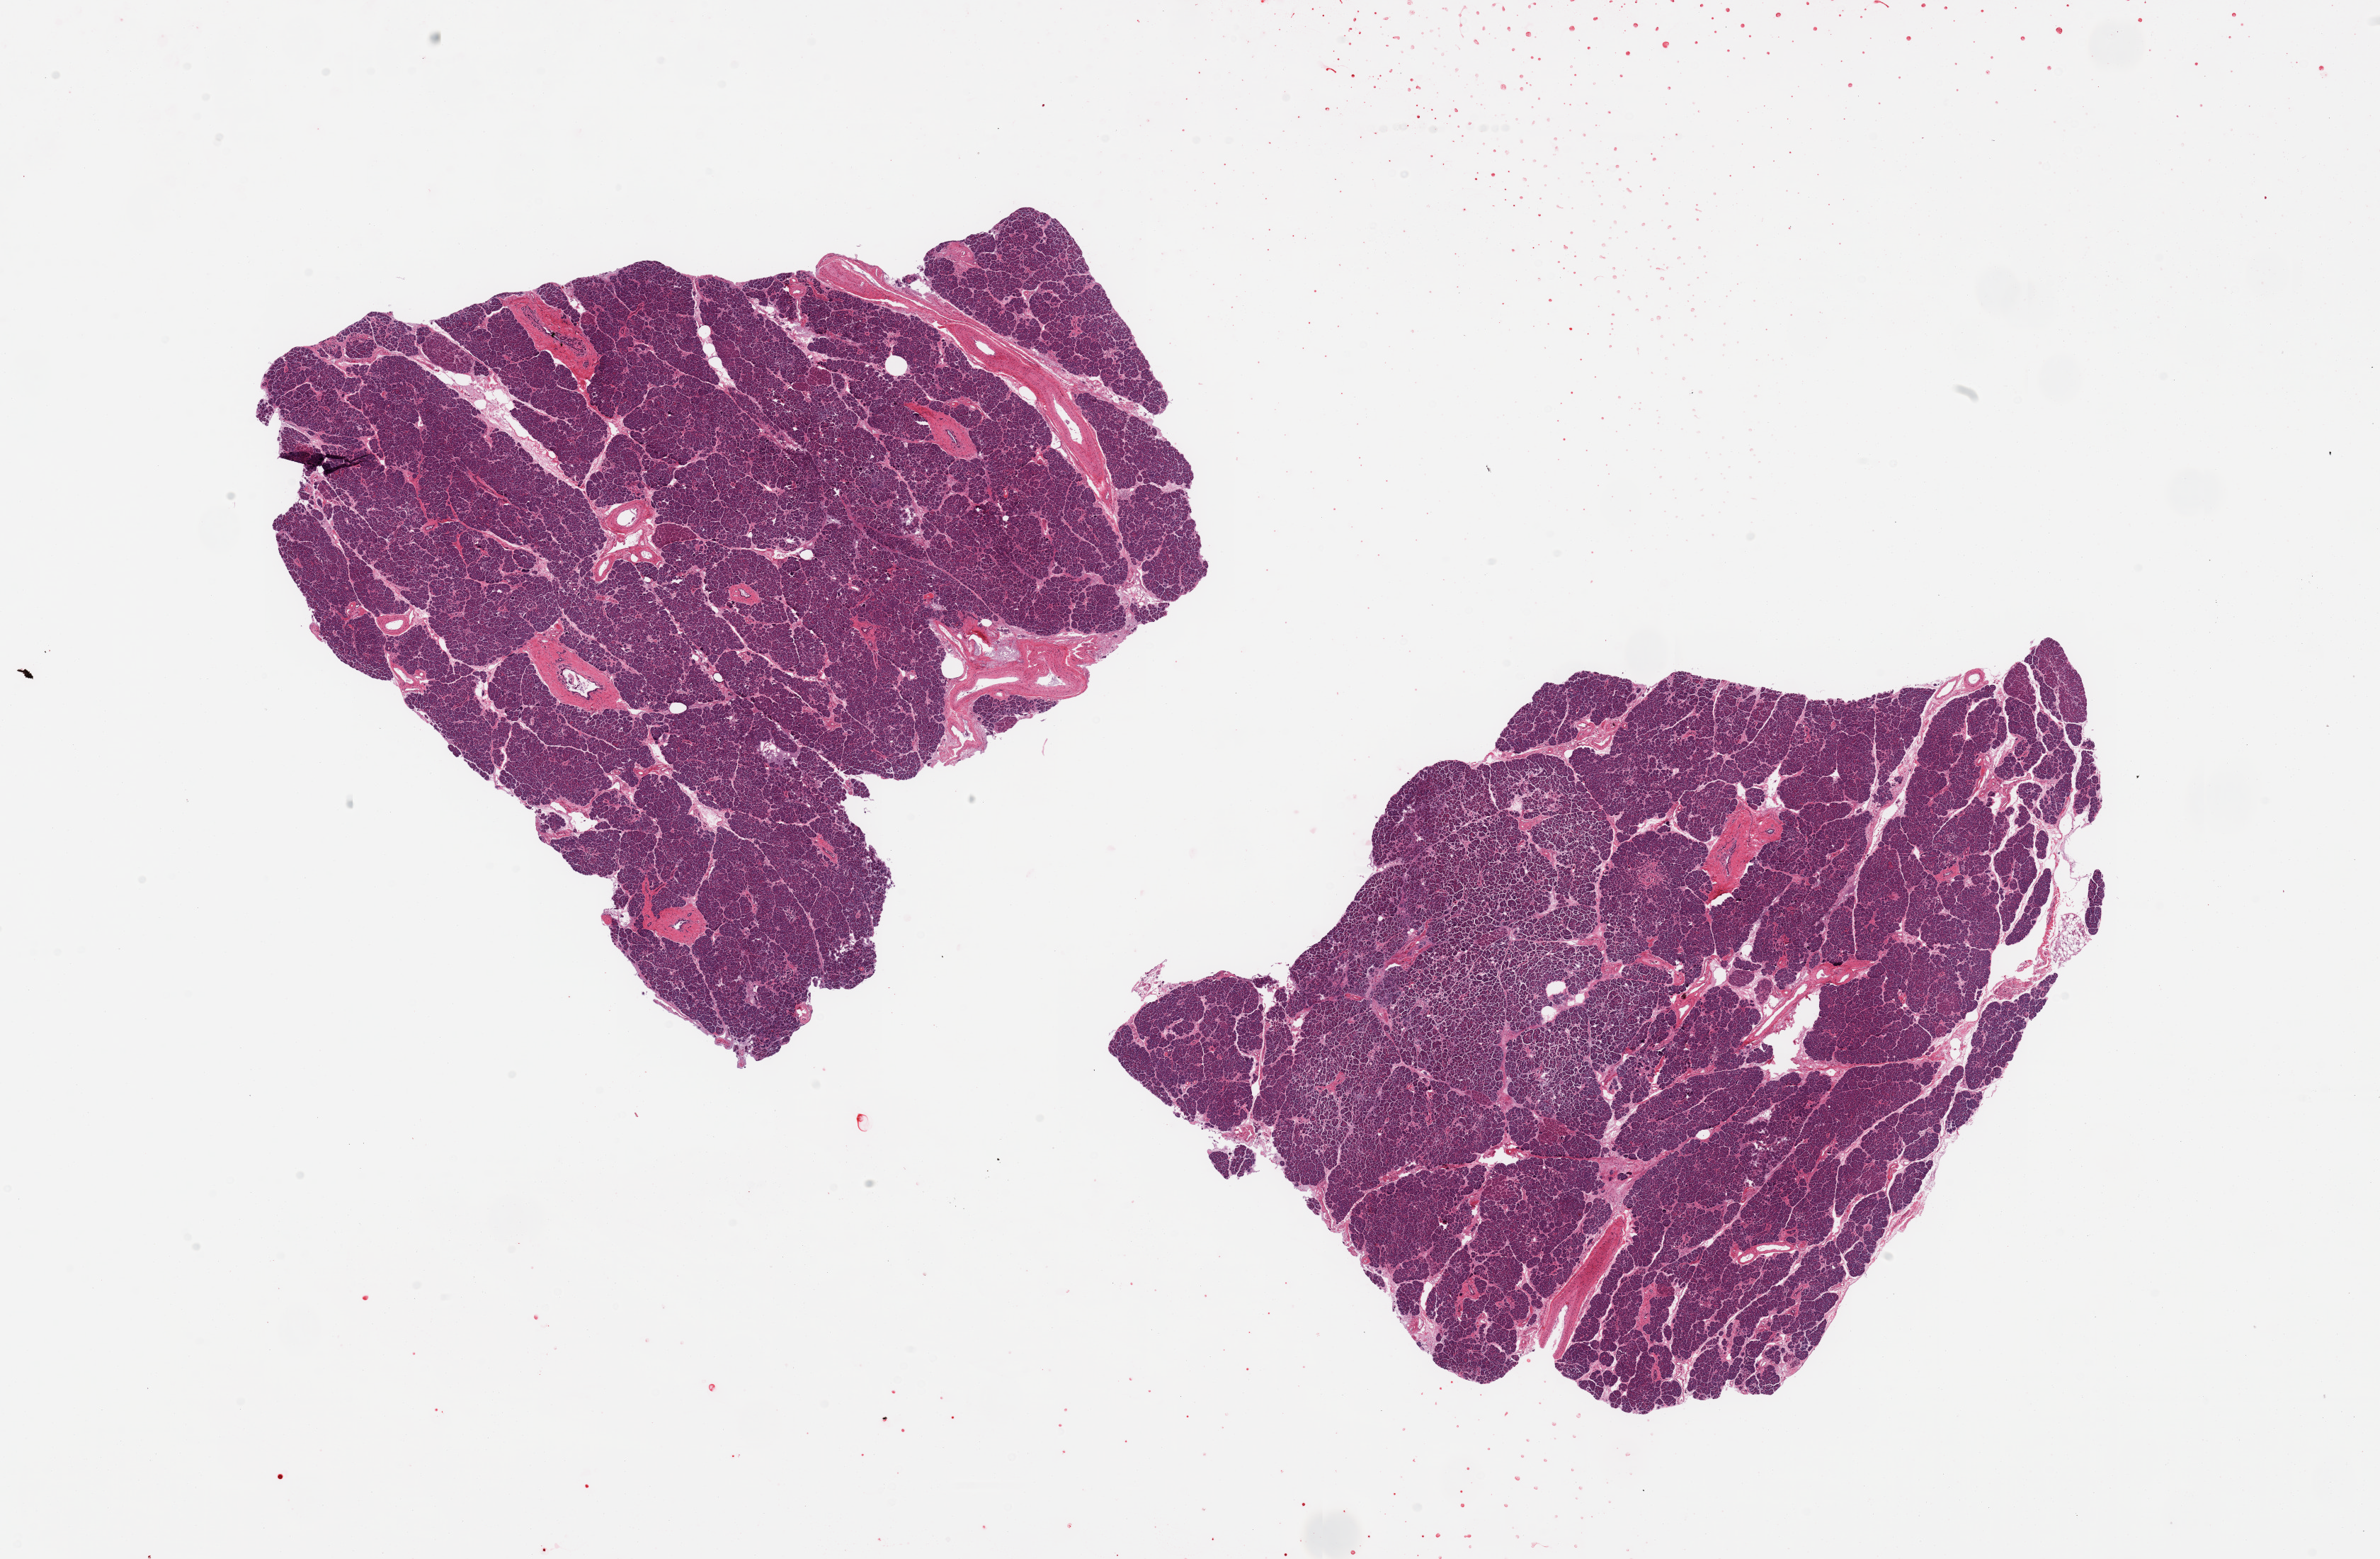
Digitized hematoxylin and eosin (H&E)-stained section, a low-resolution overview of the entire scanned area, about 26.6 x 17.4 mm (slide scanned at 20x). PAXgene-fixed paraffin-embedded (PFPE) section. Sampled site (target tissue): pancreas. Tissue donor sample.
Pathologist's review note for this sample: 2 pieces; rare Langerhans islets.